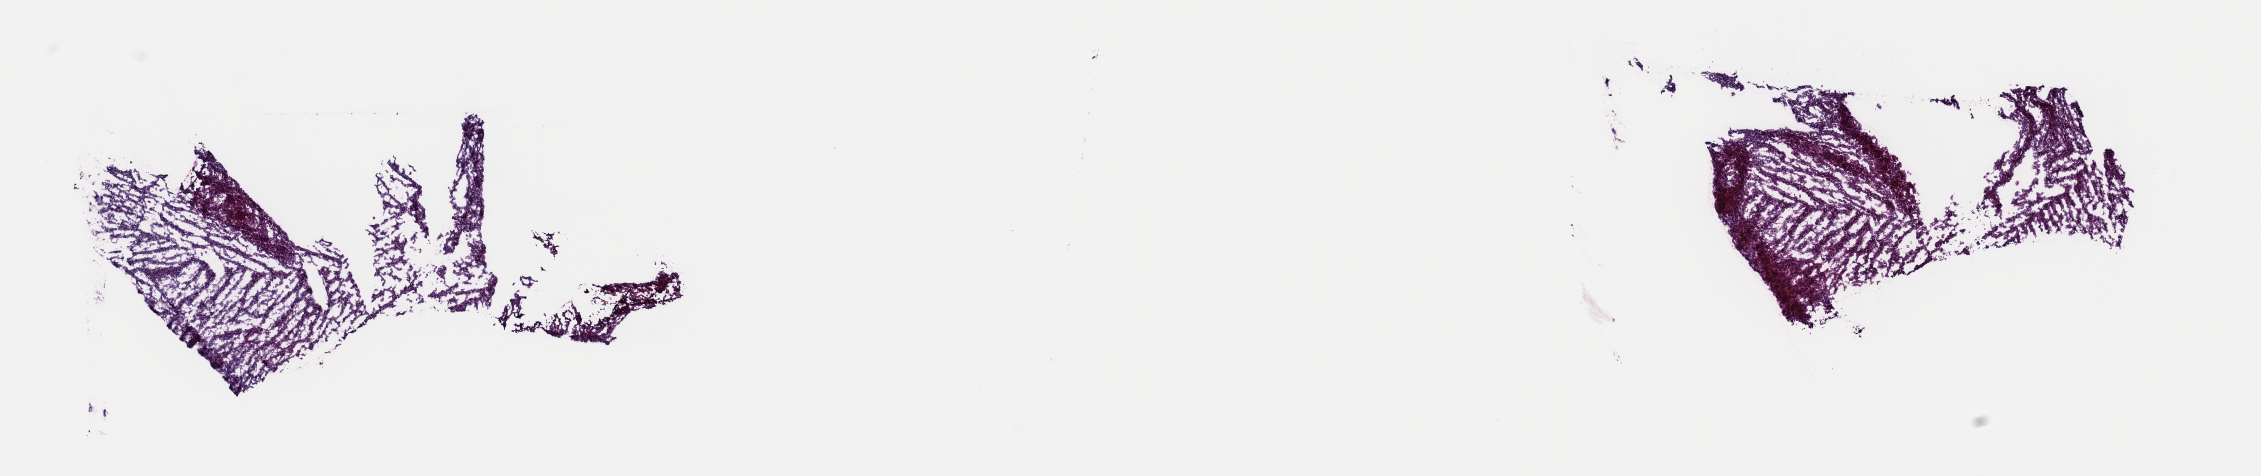
Whole-slide histology image, H&E-stained, a low-resolution overview of the entire scanned area, about 17.9 x 3.8 mm, frozen section from the top of the tissue portion, sample: primary tumour, liver. Female patient; age at initial diagnosis 61 years. Histologic grade: G1 (well differentiated). Composition of this section per pathologist review: tumour cells 100%, tumour nuclei 80%, normal cells 0%, stromal cells 0%, necrosis 0%. Infiltration values recorded for this section: lymphocyte infiltration 1%, monocyte infiltration 0%, neutrophil infiltration 0%.
Diagnosis: Hepatocellular carcinoma, NOS. AJCC pathologic stage: II (7th edition).